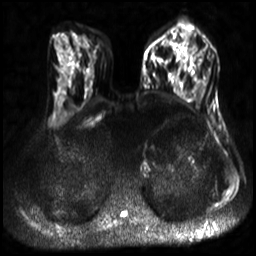
Breast MRI, one axial slice. Position 12 of 30 along the scan axis. Diffusion-weighted series; image 2 of 4 stored at this slice position (different b-values; order by instance number). 3 T. 4 mm slice thickness. 256 × 256 image matrix, field of view 320 × 320 mm. Female patient.
Structures marked on this image (expert manual segmentation):
- tumour on diffusion-weighted imaging: box from (x=191, y=38) to (x=200, y=52) px